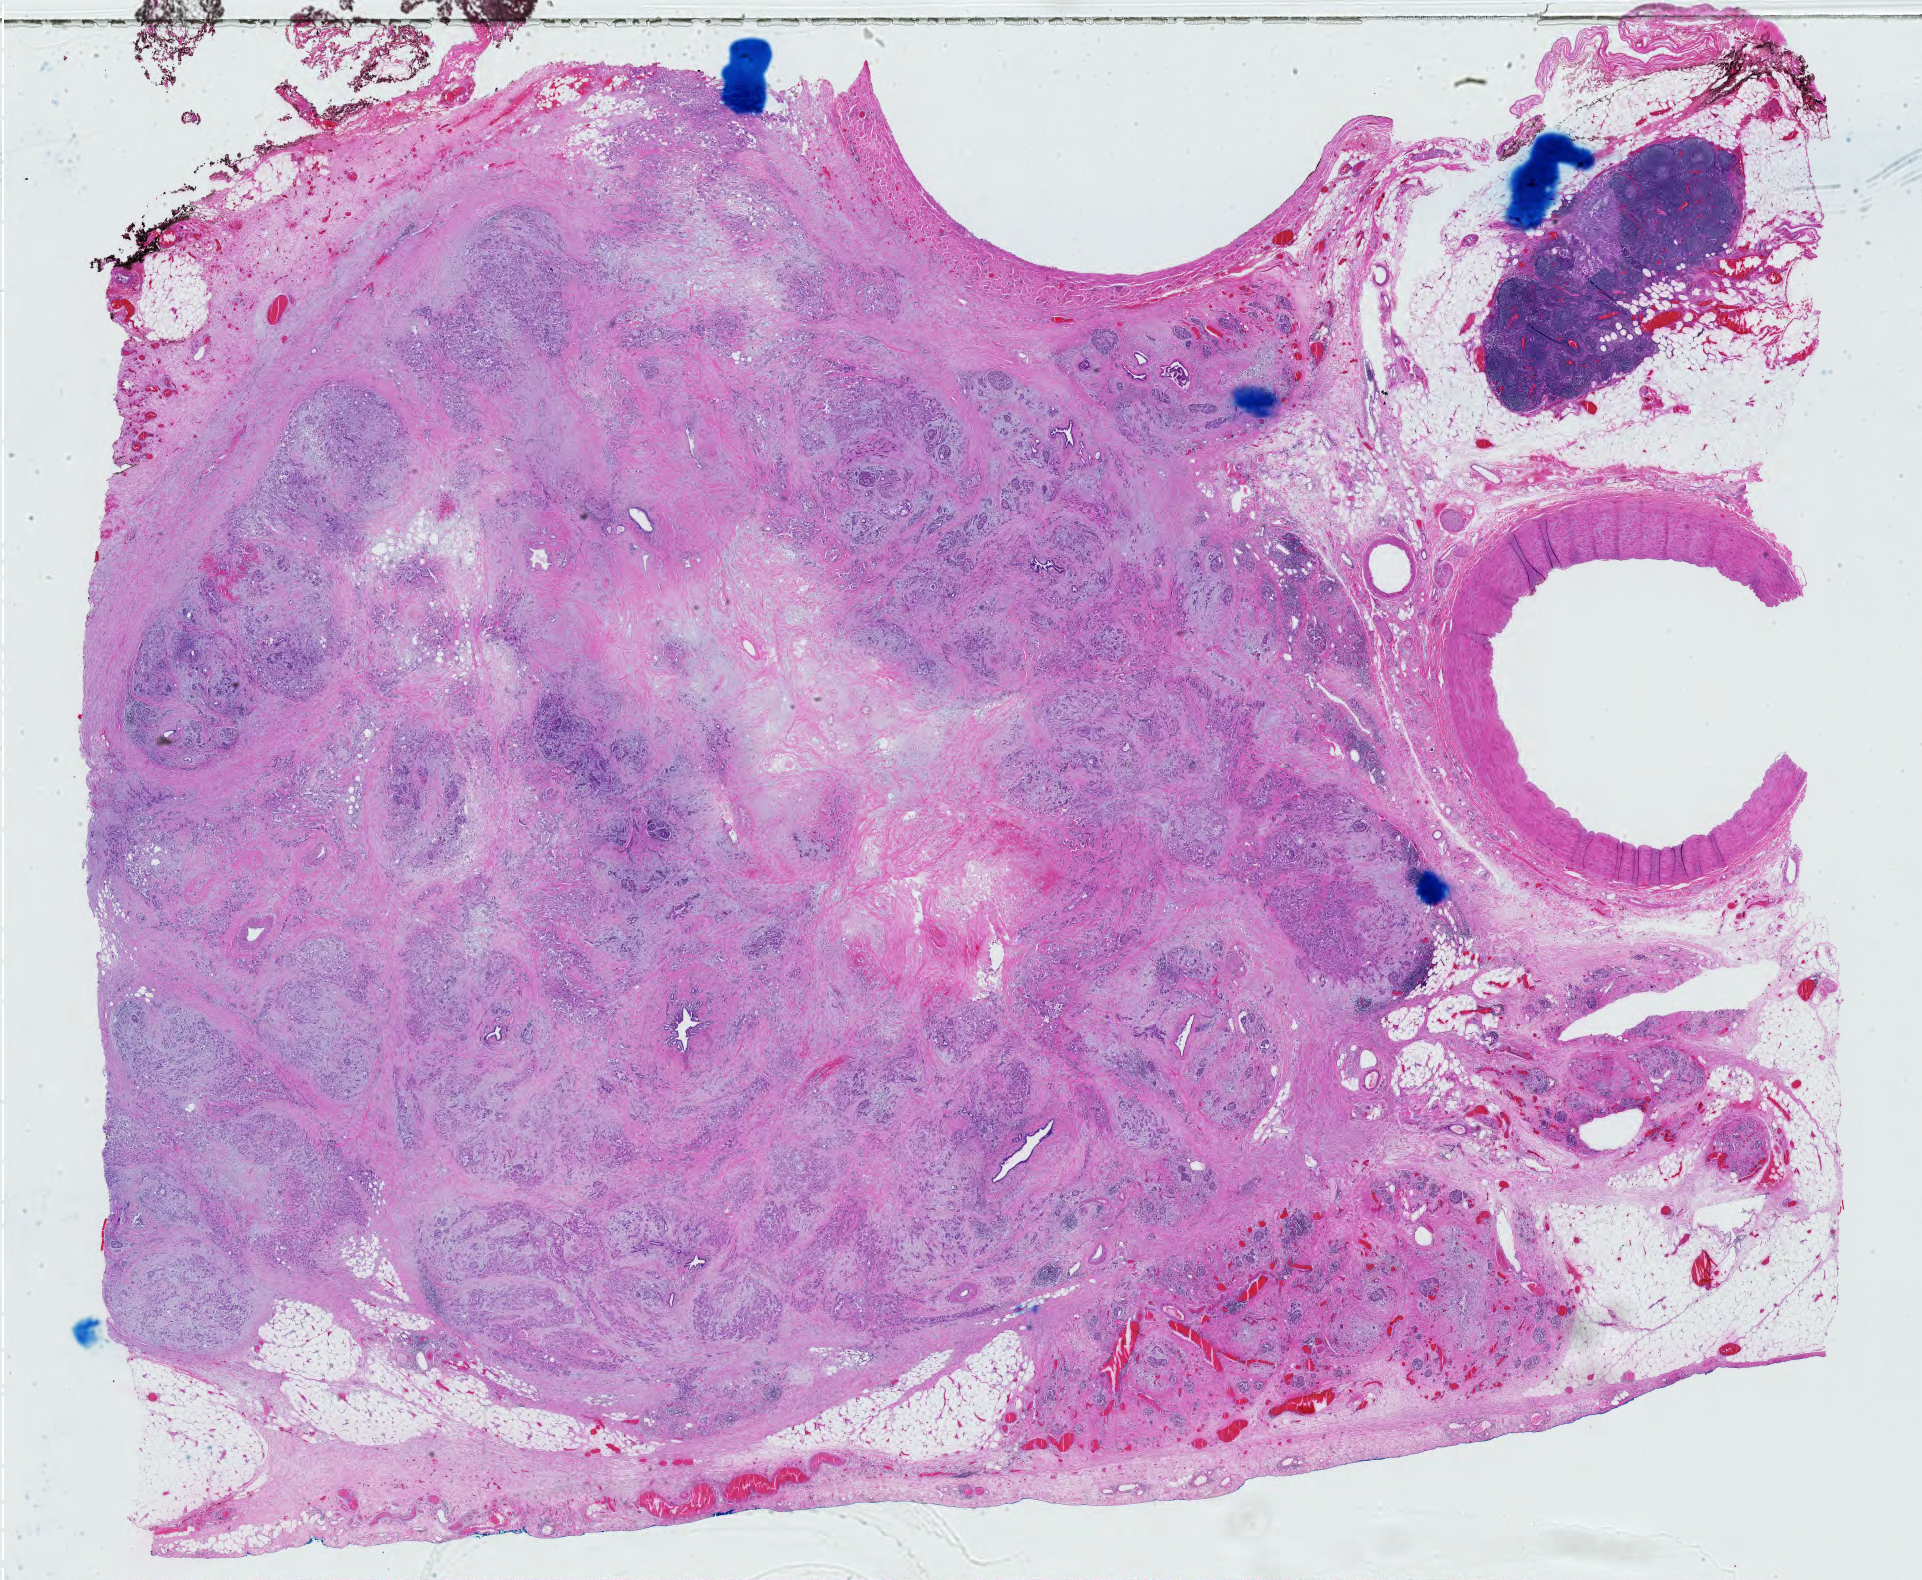
Whole-slide histology image, H&E — low-resolution overview of the scanned area, about 27.9 x 22.9 mm (slide scanned at 40x); formalin-fixed paraffin-embedded (FFPE) diagnostic section; primary tumour sample from the pancreas. Patient: male, age at initial diagnosis 43 years. Histologic grade: G3 (poorly differentiated).
Lymph nodes positive (case pathology): 1 of 9 examined. Pathologic diagnosis: Infiltrating duct carcinoma, NOS (tail of pancreas). AJCC pathologic stage: IIB (7th edition).